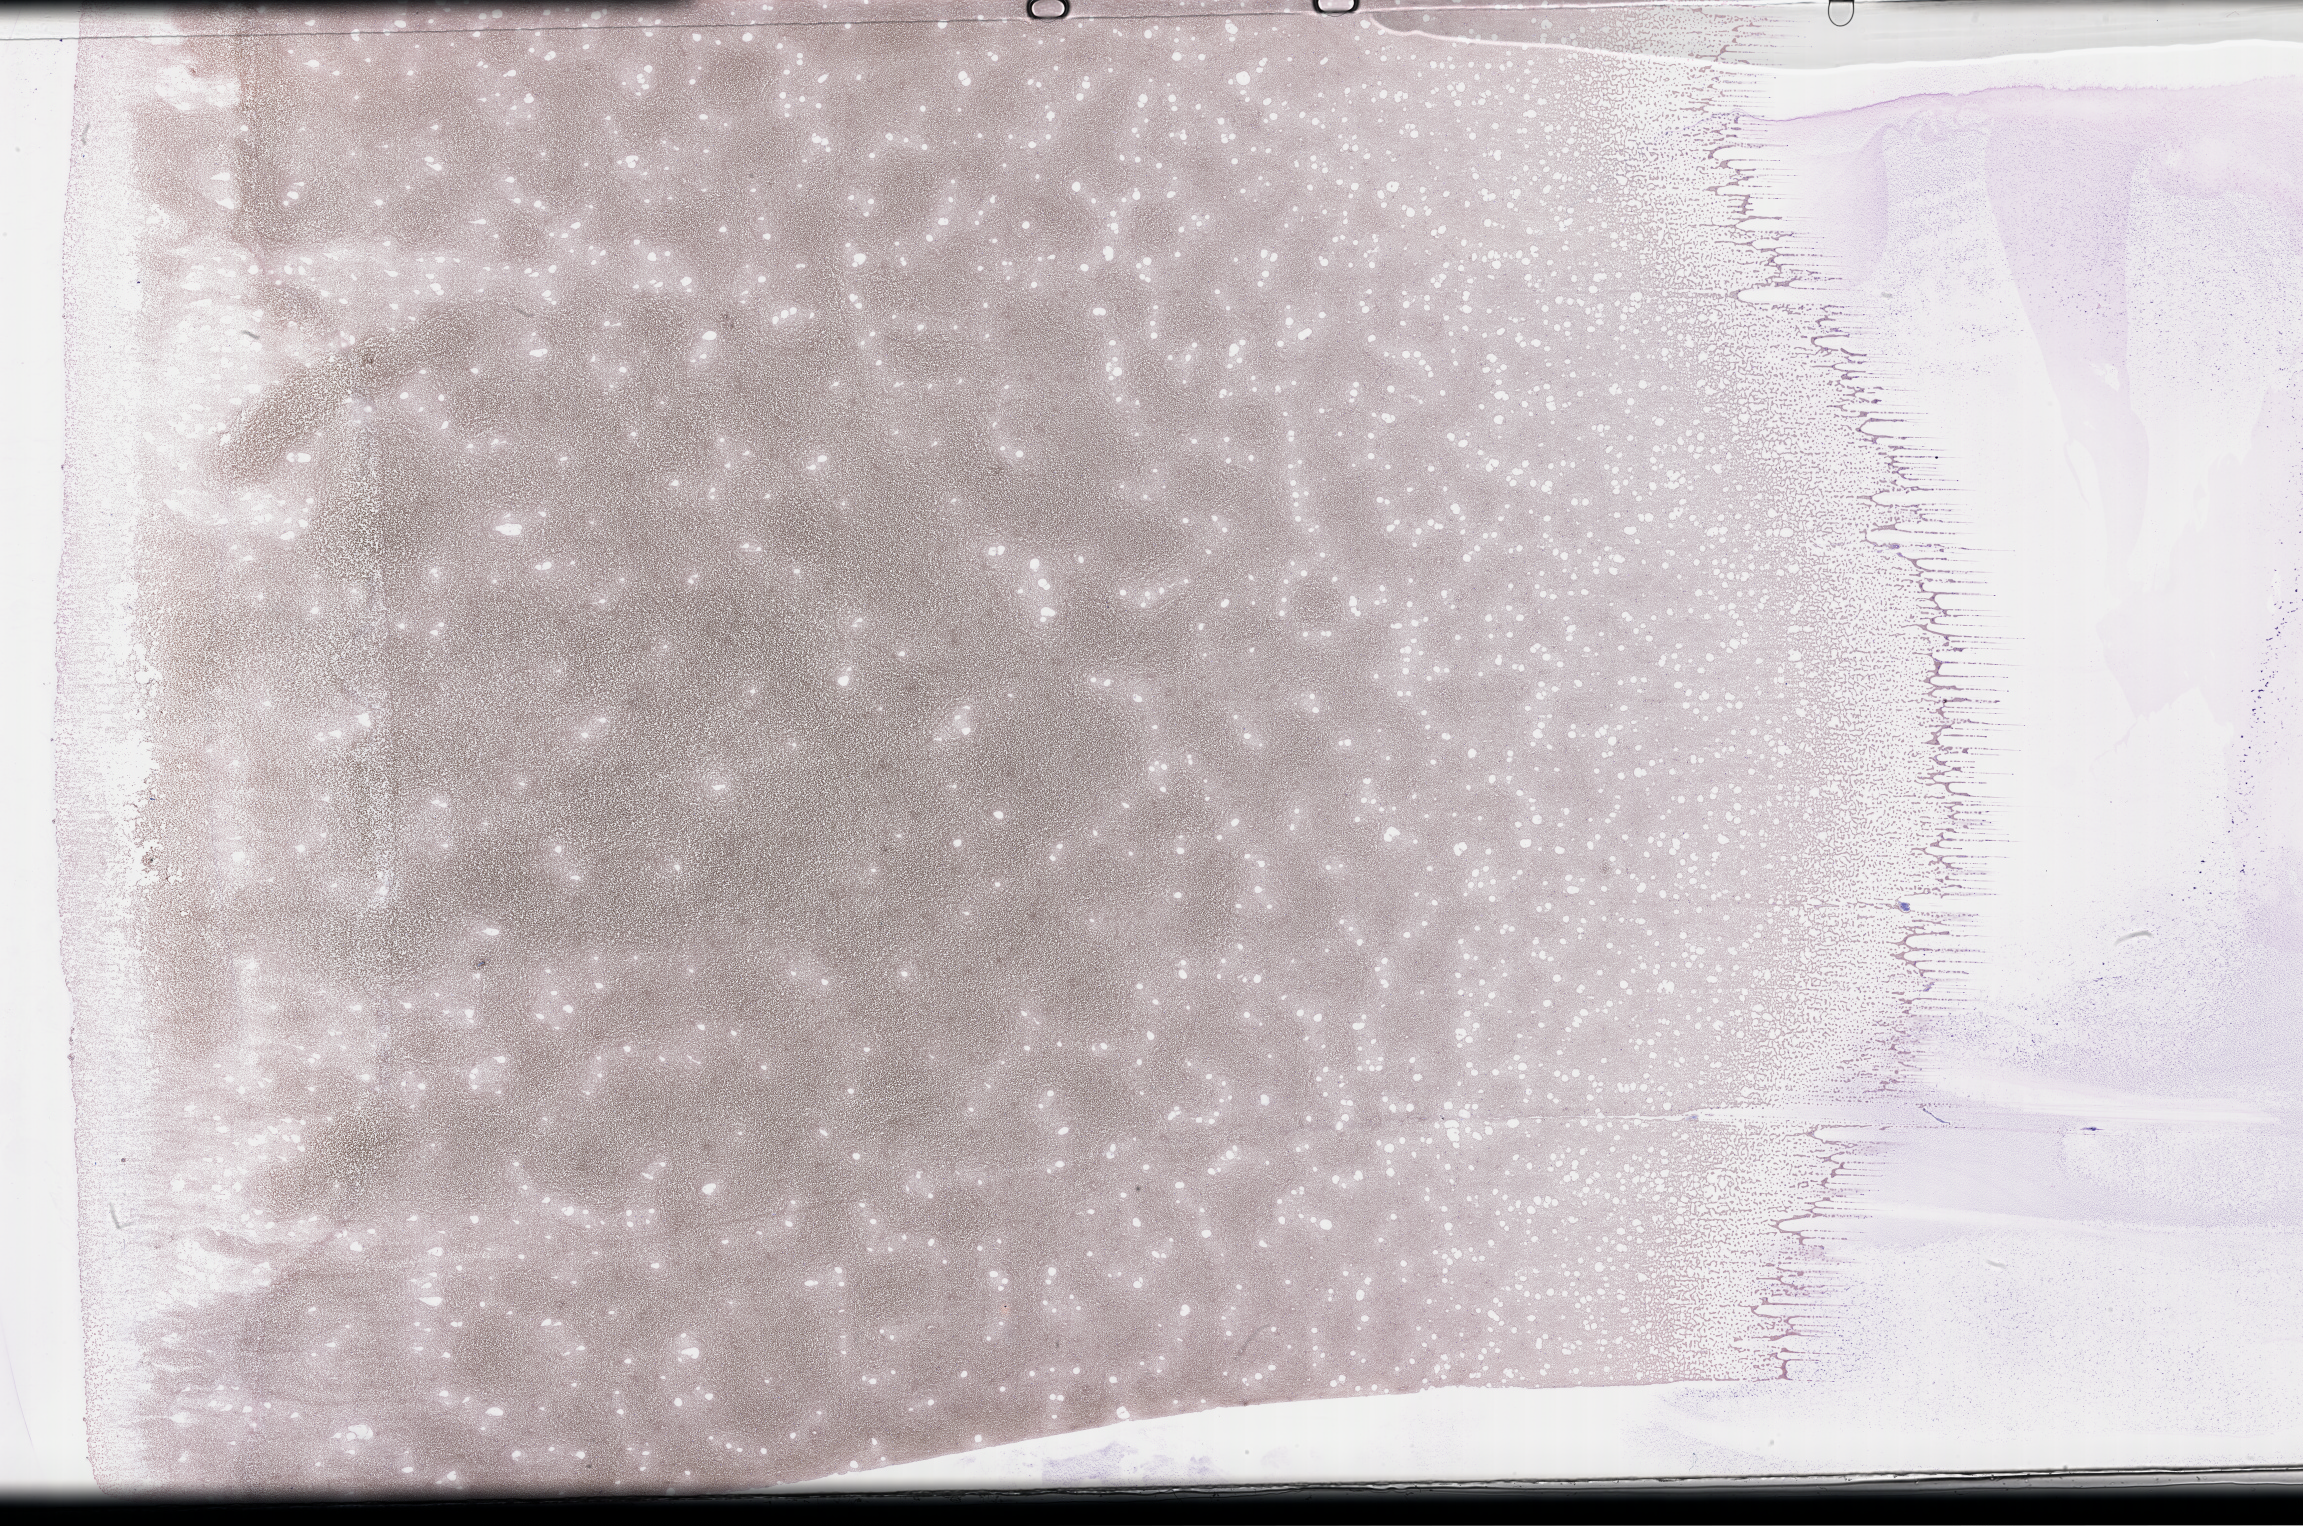
Wright–Giemsa-stained whole blood smear, whole-slide image, low-resolution overview of the scanned area, about 37.2 x 24.6 mm; collected on treatment. Patient sex: male.
From a patient with: Plasma Cell Myeloma.